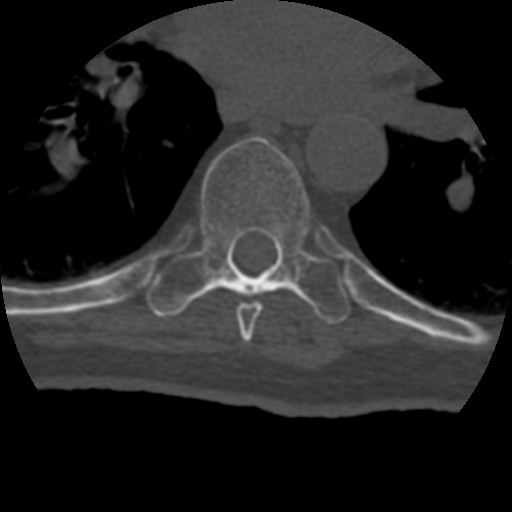
CT including the spine, one axial slice; slice 266 of 399 in the series (ordered by position); reconstruction kernel STANDARD; 120 kVp; bone window (W 1800 / L 400 HU); 1.25 mm slice thickness; 512 × 512 image matrix. Patient age 69 years. Case-level facts recorded for this patient, not image findings: primary cancer: prostate.
Outlined on this slice (semi-automatic segmentation, software-assisted and operator-edited):
- T7 vertebra: box from (x=237, y=302) to (x=263, y=341) px
- T8 vertebra: (x=147, y=137)–(x=351, y=324)